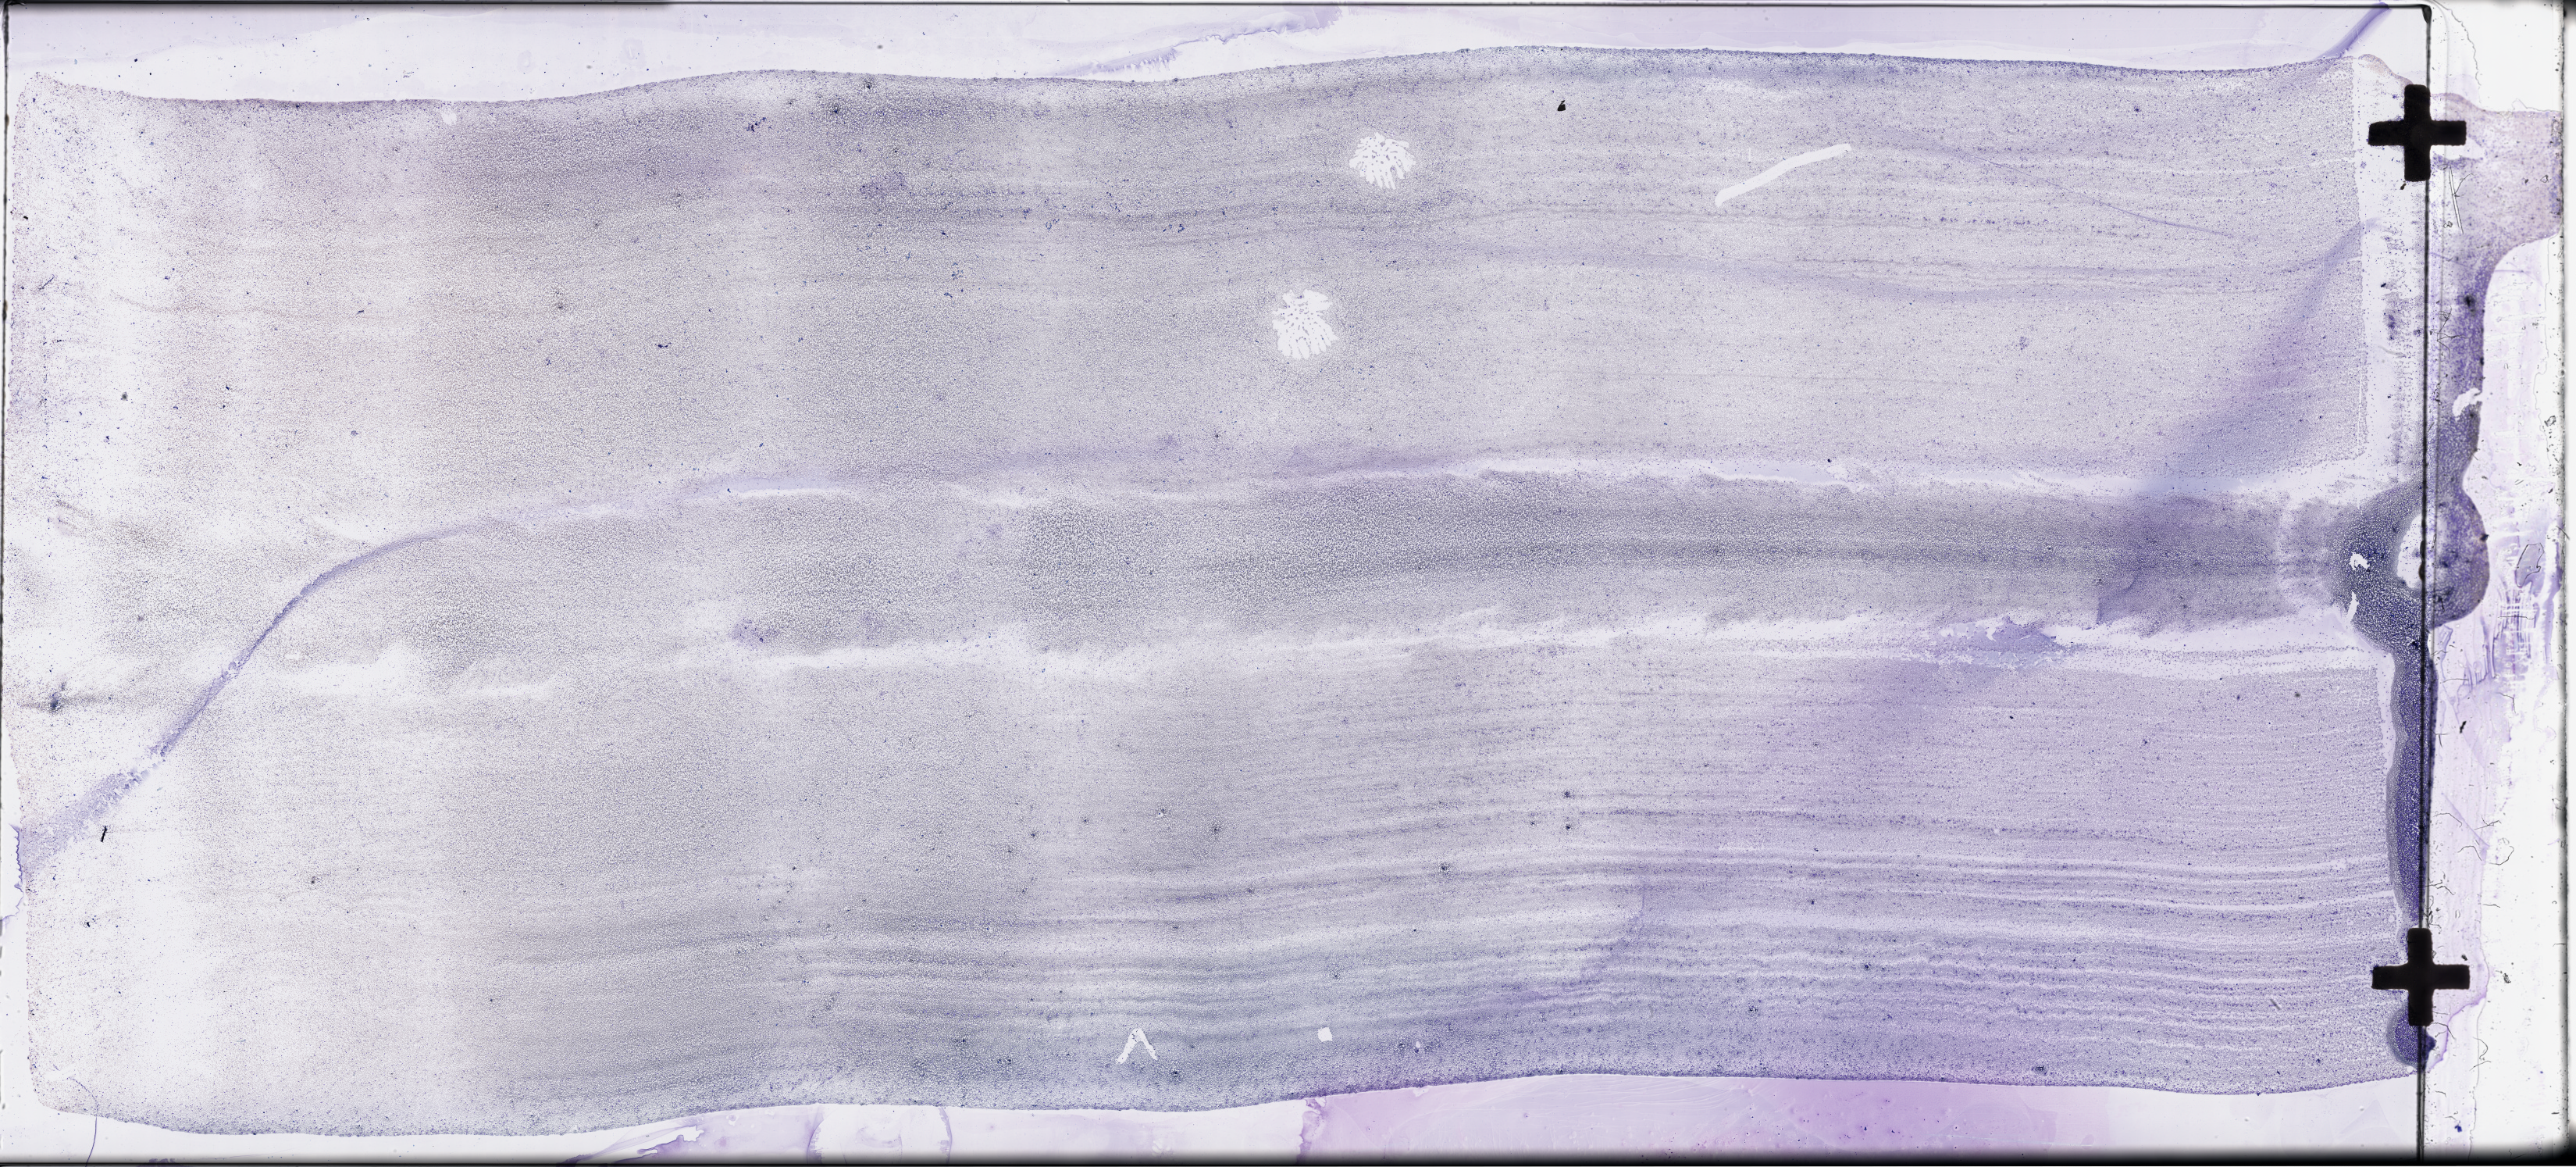
Whole-slide histology image, Hematoxylin and eosin (H&E) stained, shown as a low-resolution overview of the whole scanned area (about 53.3 x 24.1 mm, from a 40x scan). Peripheral blood (leukaemic) sample. 58-year-old female patient.
- FAB classification: M5
- WHO classification: Acute monoblastic and monocytic leukemia
- diagnosis: Acute Myeloid Leukemia